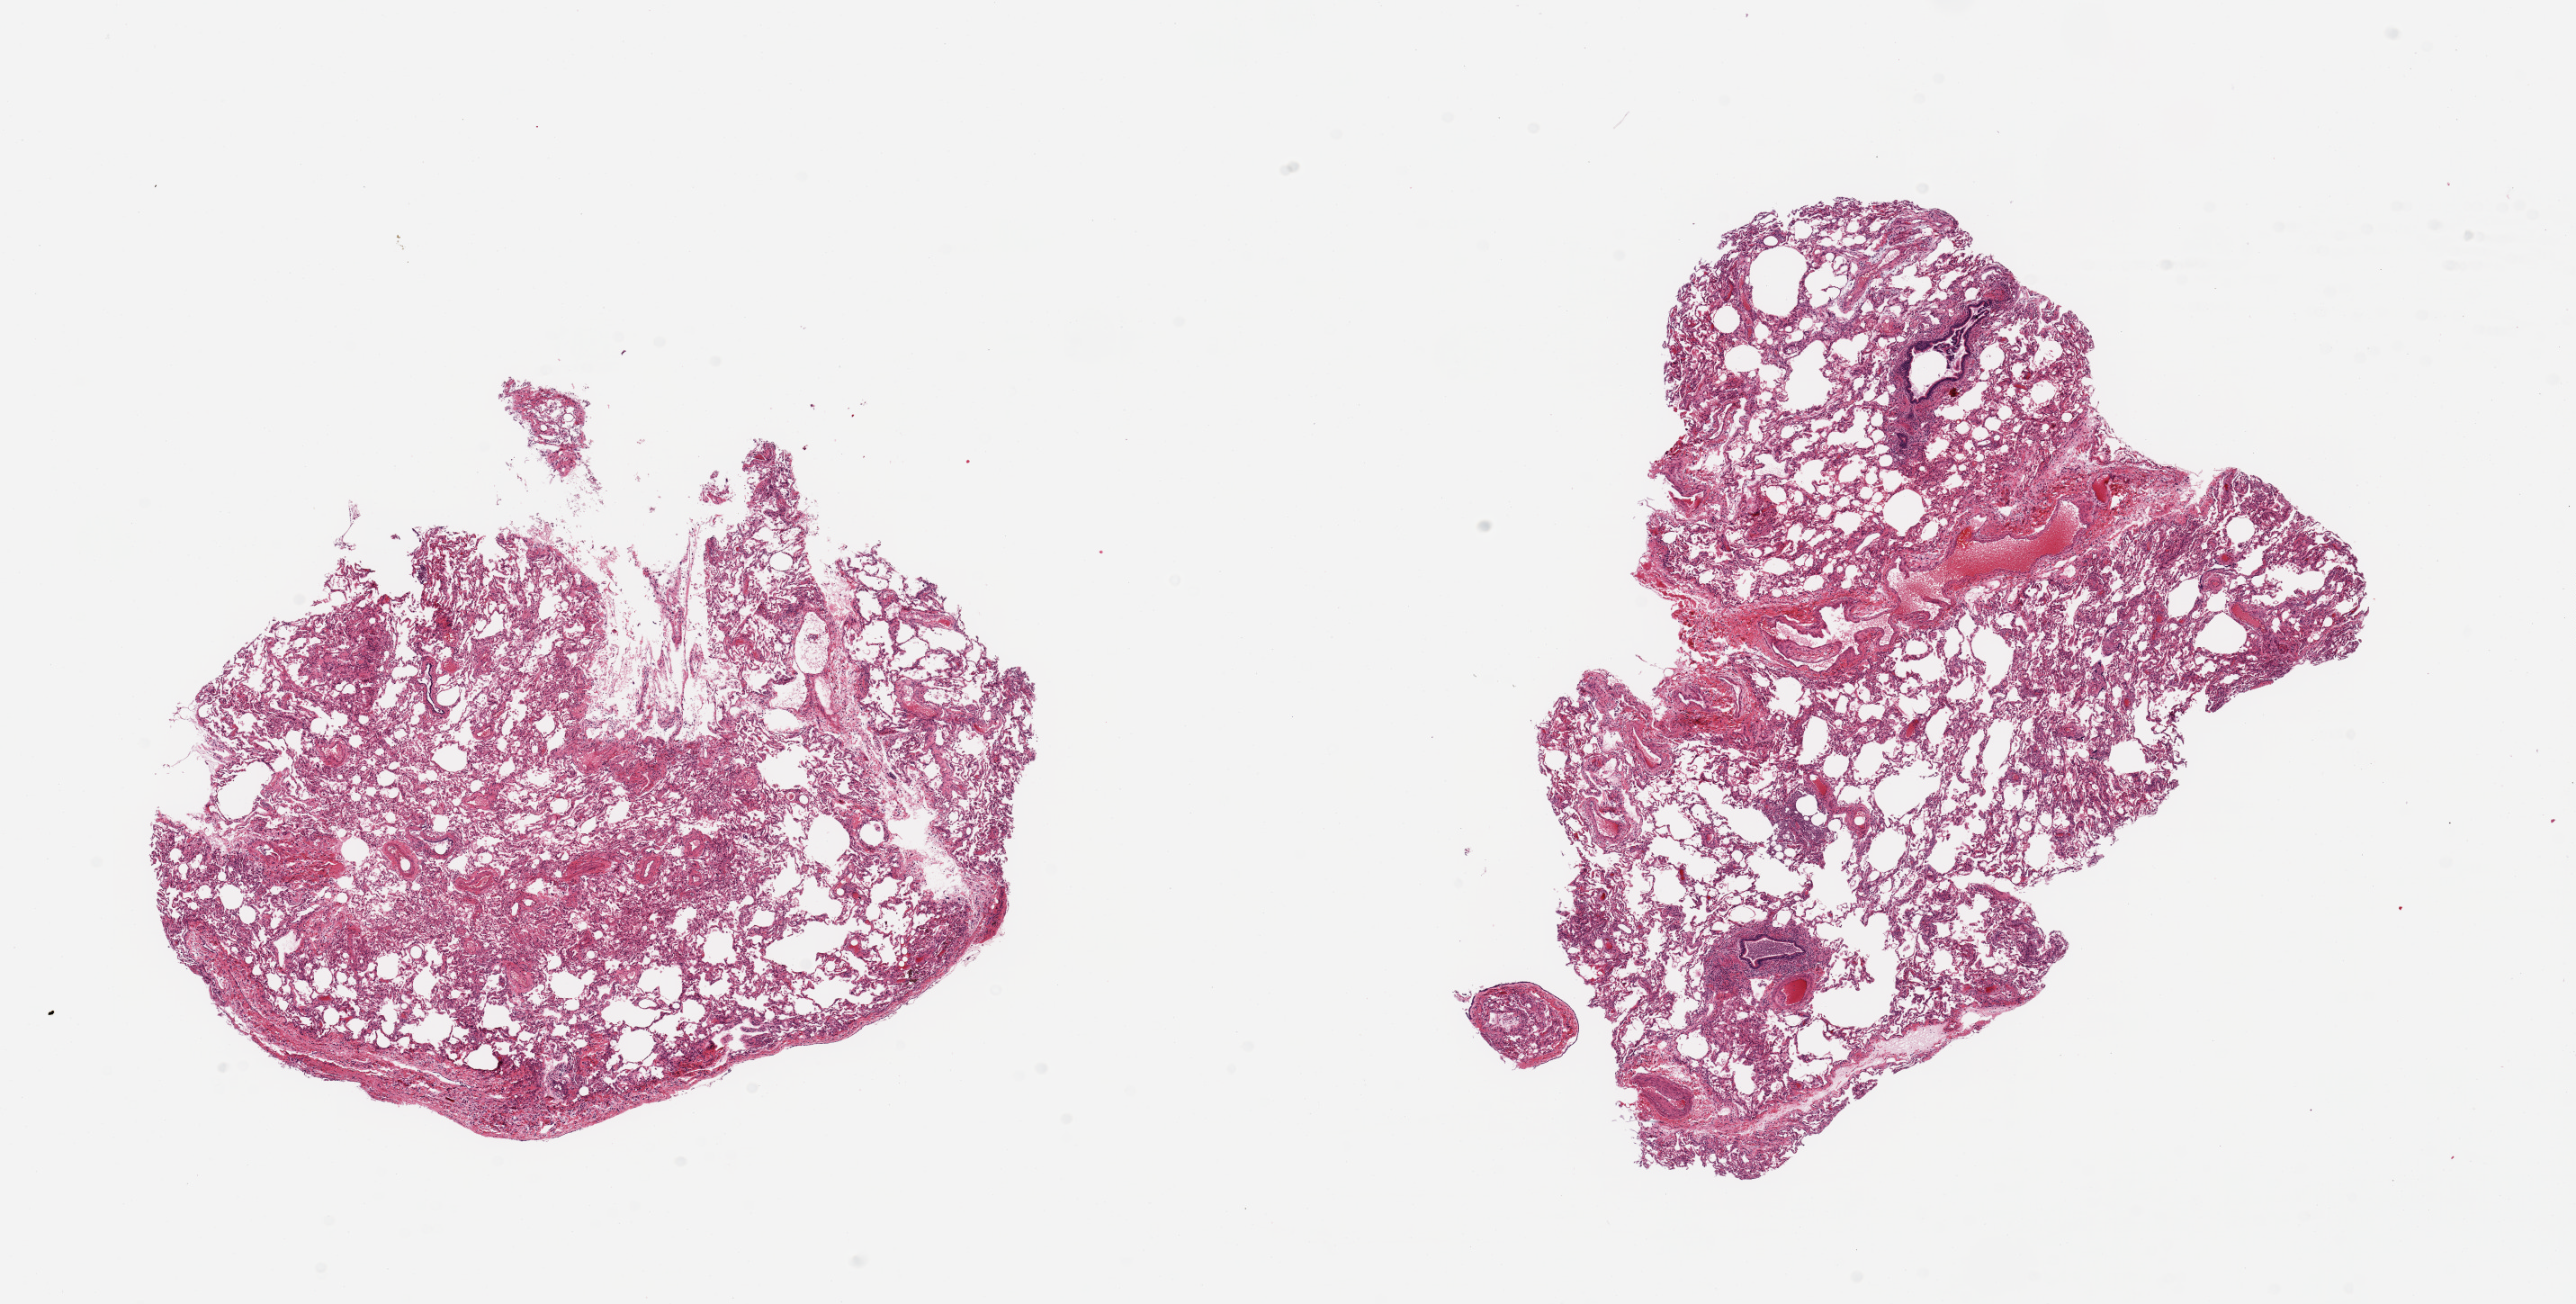
Digitized hematoxylin and eosin (H&E)-stained section, whole scanned area (about 22.6 x 11.5 mm, from a 20x scan) shown as a low-resolution overview; PAXgene-fixed, paraffin-embedded tissue; sampled site (target tissue): lung; tissue donor sample. Donor: male.
• pathologist's review note for this sample: 2 pieces, minimal congestion